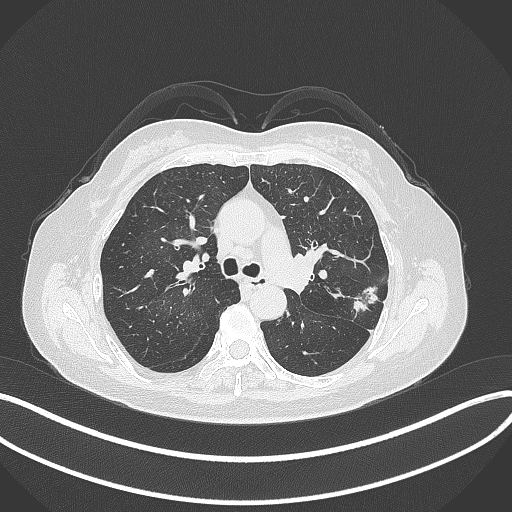
Chest CT, one axial slice. Position 207 of 319 along the scan axis. Lung window (W 1500 / L -600 HU). 1 mm slice thickness. 512 × 512 image matrix, field of view 400 × 400 mm. Patient: female, 60 years. From the clinical record (not read from this slice): clinical TNM (as recorded): T1c N0 M0.
Structures marked on this image (bounding box drawn by a radiologist):
- lung tumour (recorded histology: adenocarcinoma): bounding box (x1, y1, x2, y2) in pixels: (350, 282, 379, 323)